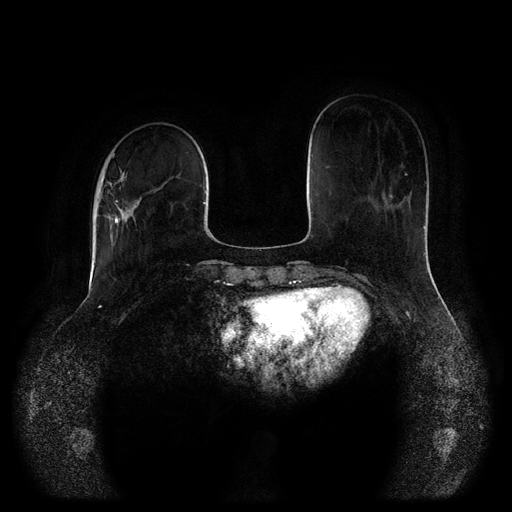
Breast MRI (dynamic contrast-enhanced, multi-phase), one axial slice. Slice 30 of 116 in the series (ordered by position). Dynamic contrast-enhanced series, time point 2 of 5 at this slice position (early post-contrast). 1.5 T. TE 2.6 ms, TR 5.2 ms. 2 mm slice thickness. 512 × 512 image matrix, field of view 380 × 380 mm. Female patient, age 52 years.
Annotated regions visible in this slice (semi-automatic segmentation, software-assisted and operator-edited):
- breast lesion (labelled 'tumour' in the annotation; benign lesions carry a separate 'benign' label): bounding box (x1, y1, x2, y2) in pixels: (105, 171, 144, 250)